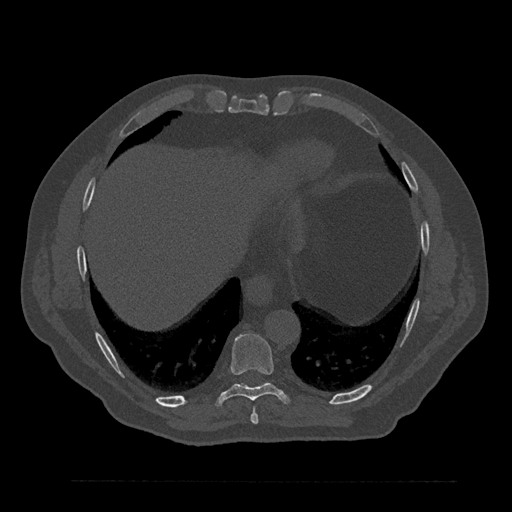
CT including the spine, one axial slice. Position 402 of 797 along the scan axis. Reconstruction kernel Br40s/3. 120 kVp. Bone window (W 1800 / L 400 HU). 0.5 mm slice thickness. 512 × 512 image matrix. Patient: male, 61 years. Case-level facts recorded for this patient, not image findings: primary cancer: prostate.
Annotated regions visible in this slice (semi-automatically segmented with operator editing):
- T8 vertebra: bounding box [x1, y1, x2, y2] px = [250, 408, 259, 425]
- T9 vertebra: [215, 333, 289, 407]